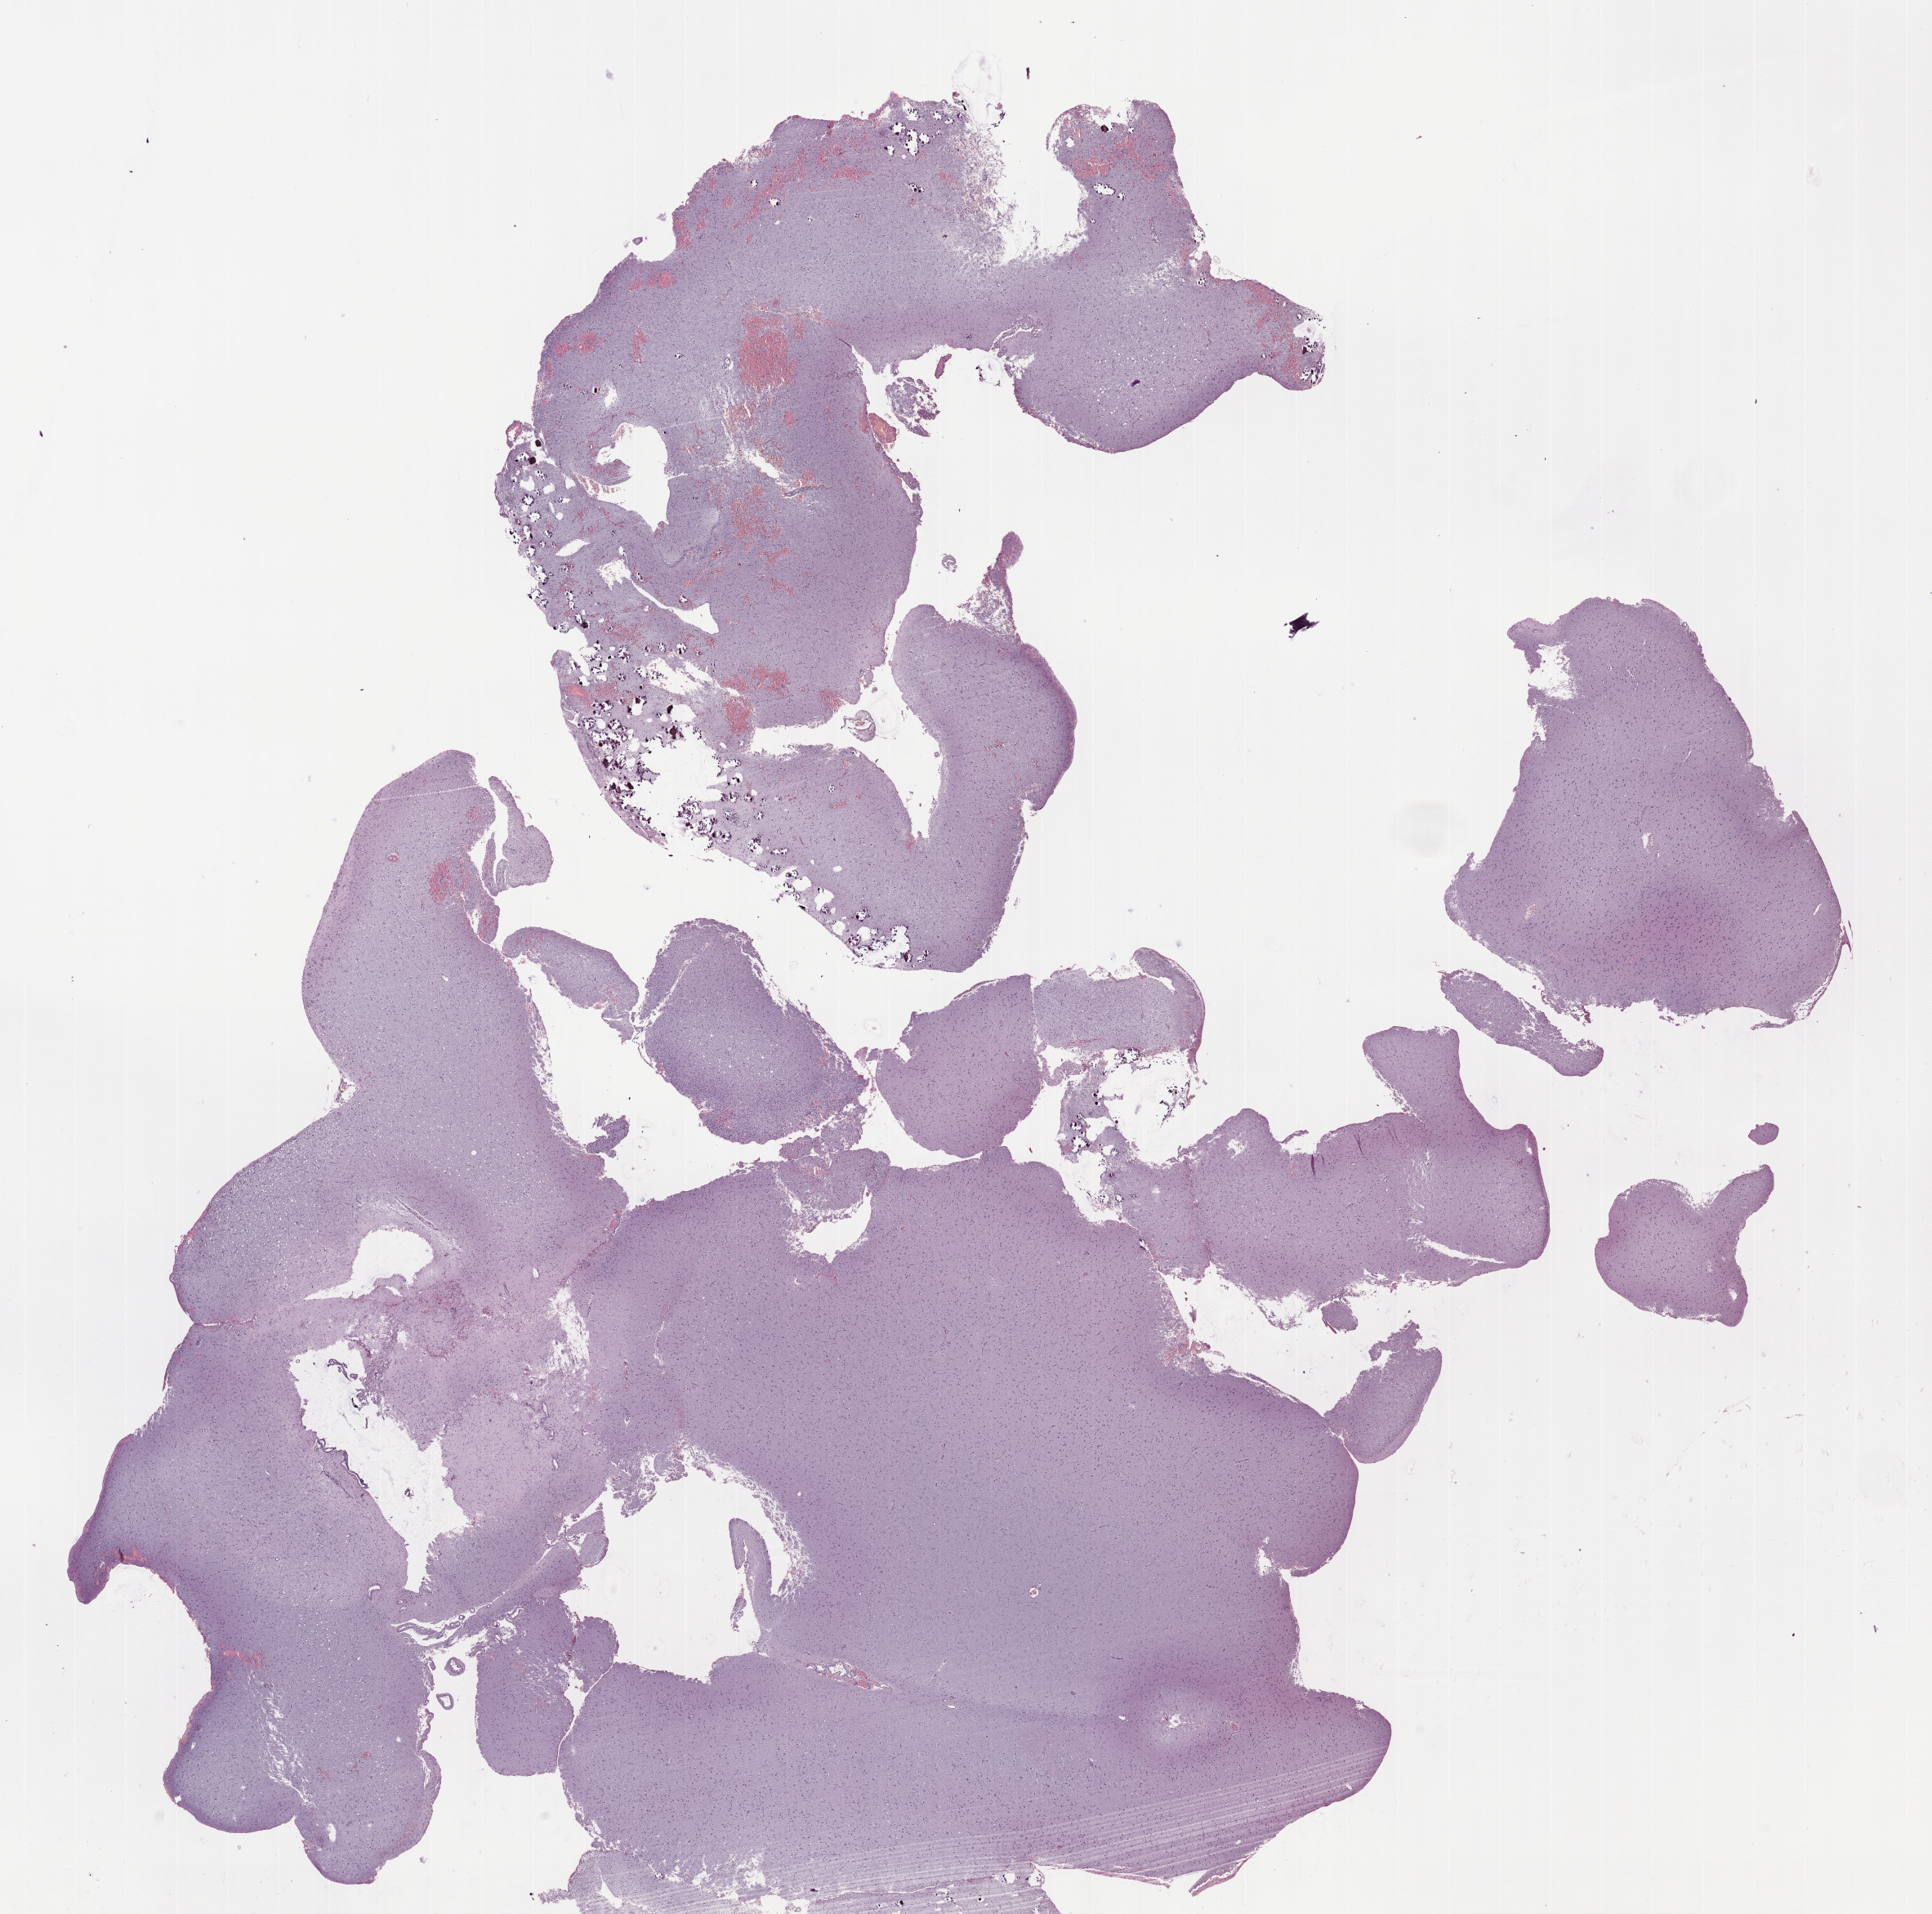
Whole-slide histology image, Hematoxylin and eosin (H&E) stained — low-resolution overview of the scanned area, about 19.1 x 18.9 mm (slide scanned at 40x). Formalin-fixed paraffin-embedded (FFPE) diagnostic section. Primary tumour sample from the brain. Patient: female, age at initial diagnosis 59 years. Histologic grade: G2 (moderately differentiated).
Laterality: right. Pathologic diagnosis: Mixed glioma (cerebrum).